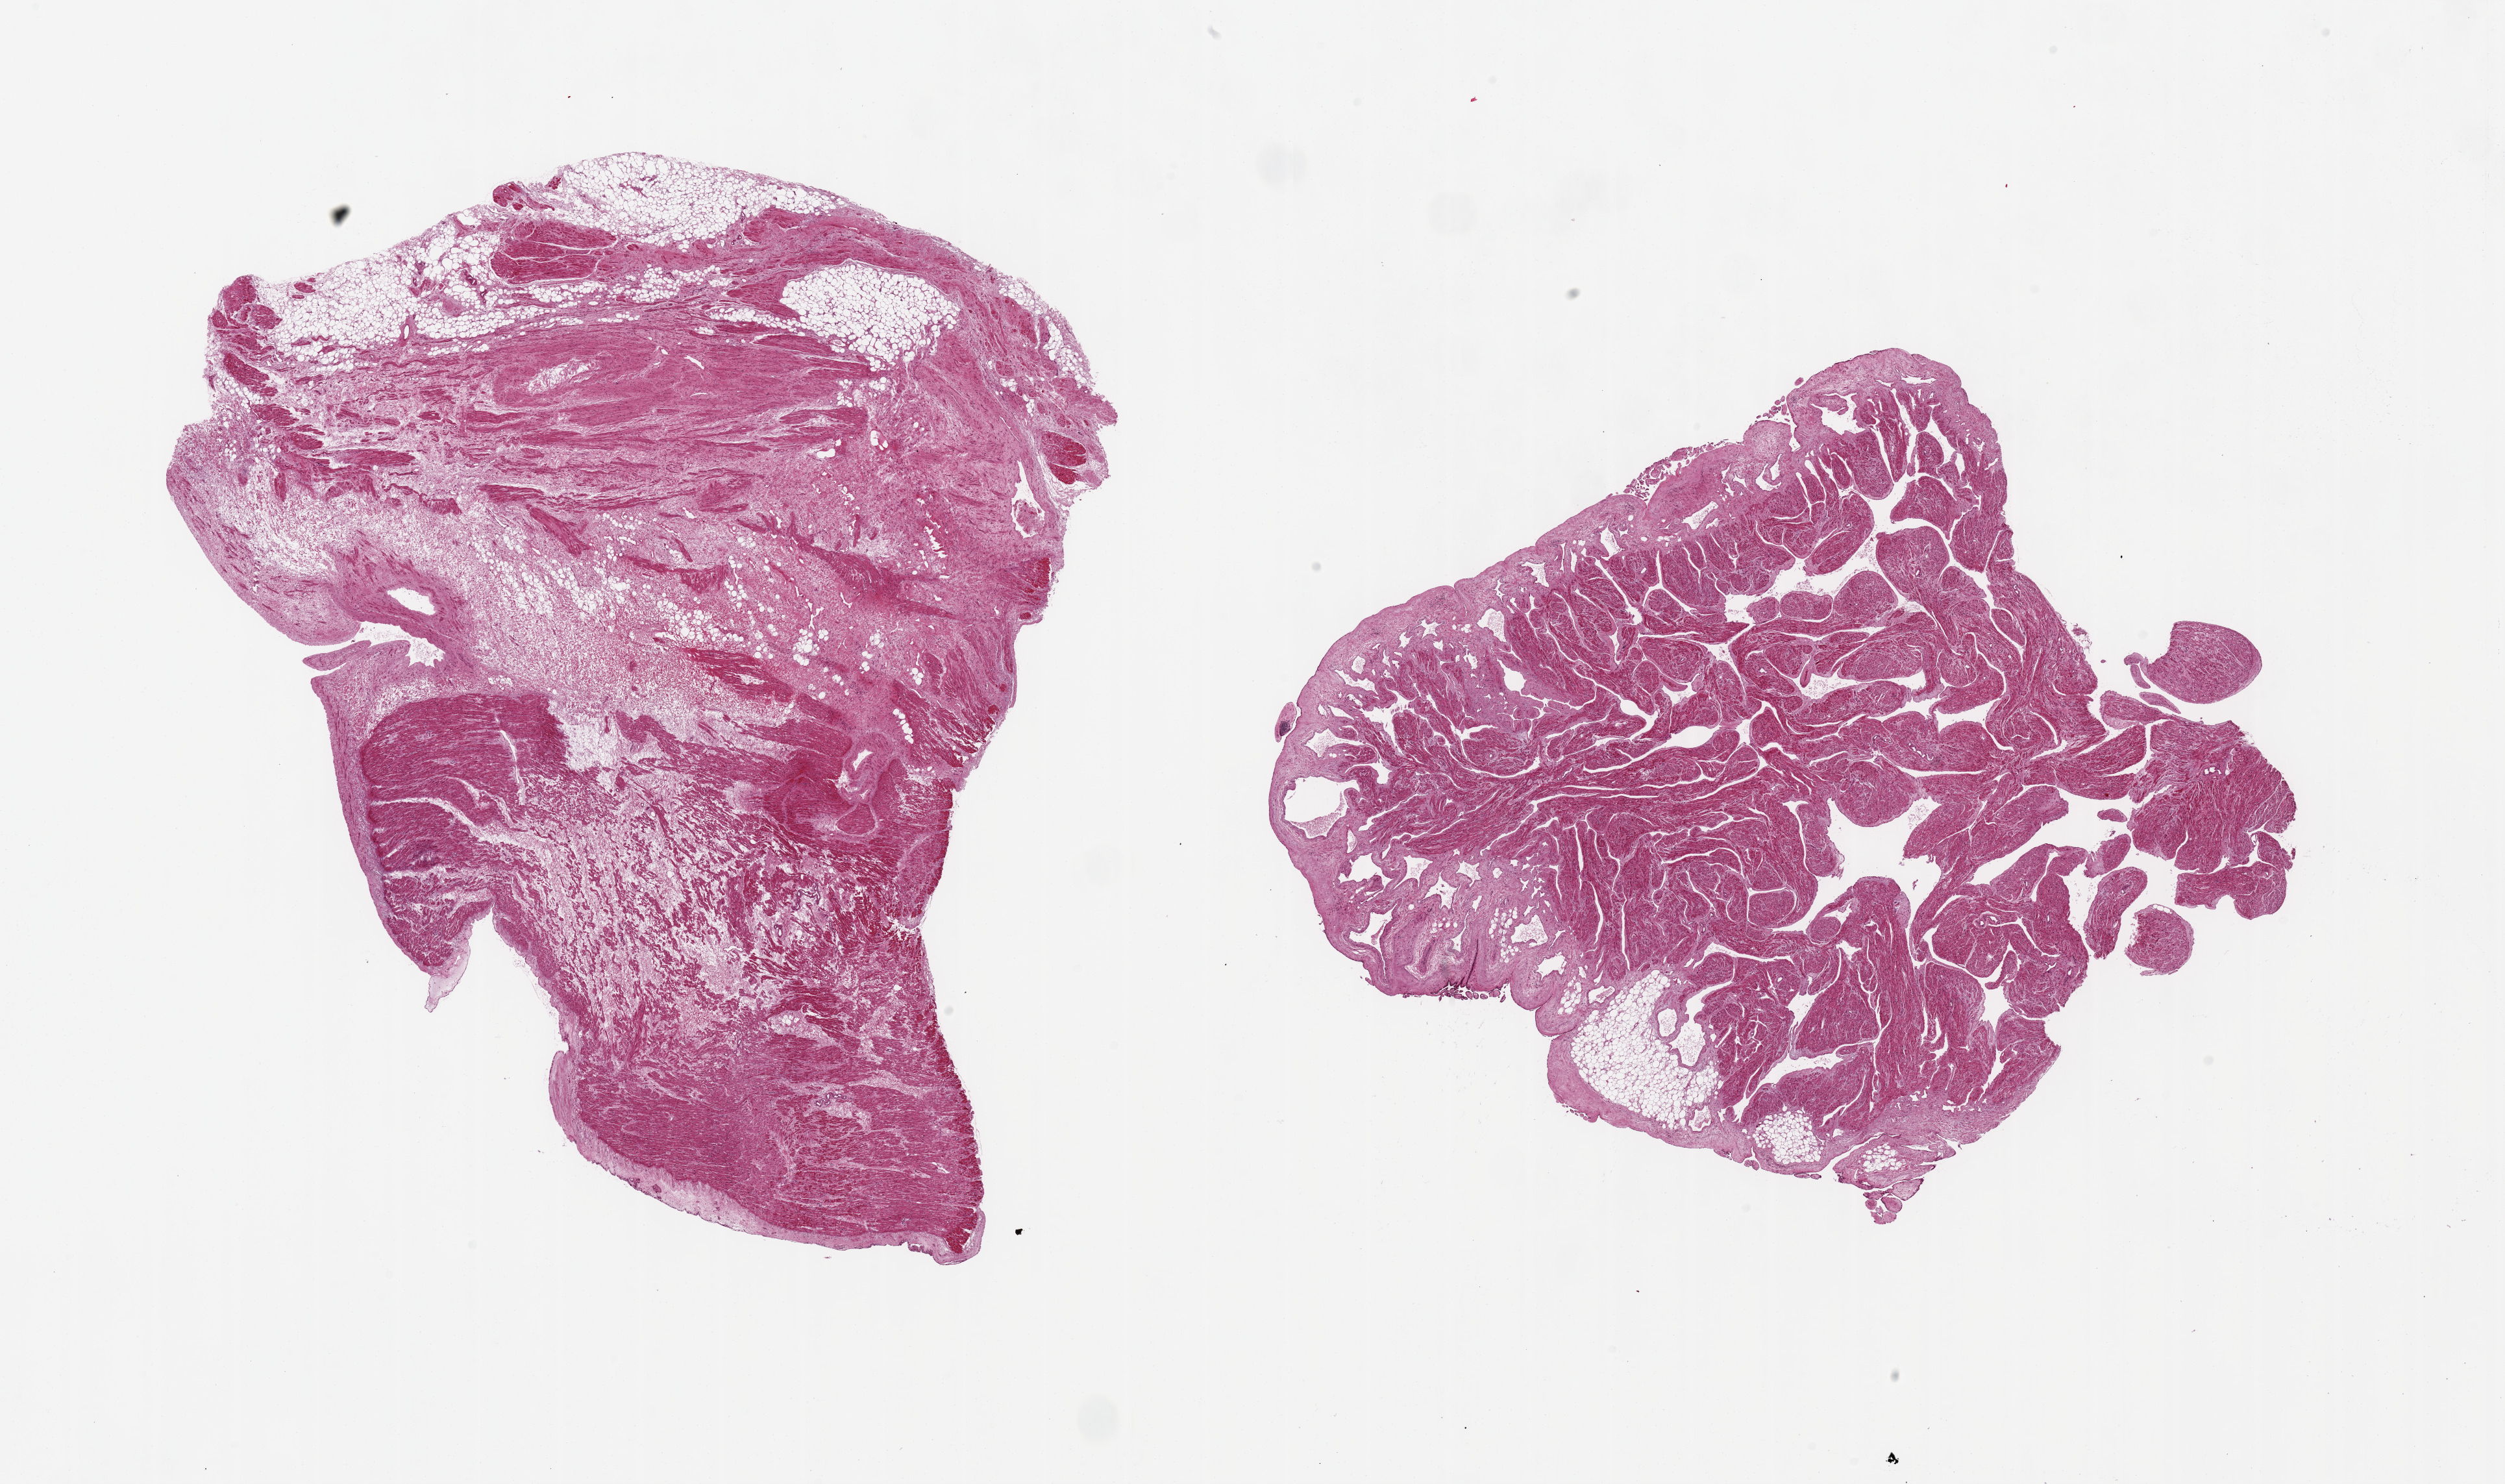
Hematoxylin and eosin (H&E) whole-slide image, a low-resolution overview of the entire scanned area, about 30.5 x 18.1 mm (from a 20x scan); PAXgene-fixed paraffin-embedded (PFPE) section; target tissue: auricular appendage; tissue donor sample. Donor sex: female.
Reviewer comment on this tissue sample: 2 pieces, 14x12 & 11x10mm; muscle content <50% in one due to fibroadipose interstitium; muscle 70% in other.